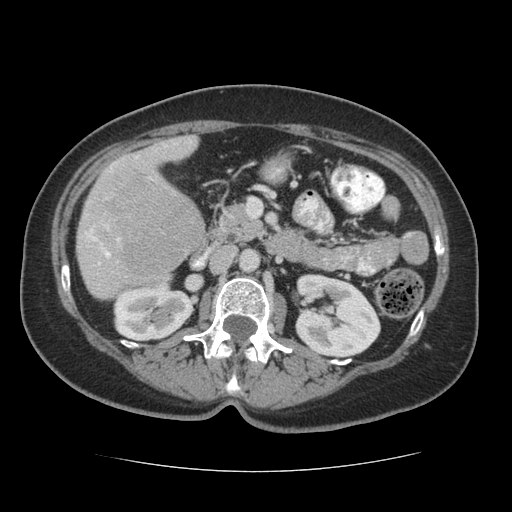
Contrast-enhanced abdominal CT (liver protocol), one axial slice. Position 19 of 75 along the scan axis. Reconstruction kernel STANDARD. 140 kVp. Soft-tissue window (W 400 / L 40 HU). 512 × 512 image matrix, field of view 360 × 360 mm. Case-level facts recorded for this patient, not image findings: diagnosis: hepatocellular carcinoma (patient treated with transarterial chemoembolisation; whether this scan precedes or follows treatment is not stated here); TNM stage (as recorded): Stage-I; Child-Pugh class: A; tumour differentiation: moderately differentiated.
Structures marked on this image (semi-automatic segmentation, software-assisted and operator-edited):
- liver parenchyma outside the tumour (the mass and vessels are separate outlines, so this box may not span the whole liver): bounding box <76,134,204,298> (left, top, right, bottom; pixels)
- mass: <99,165,203,280>
- liver vessels: <84,143,176,265>